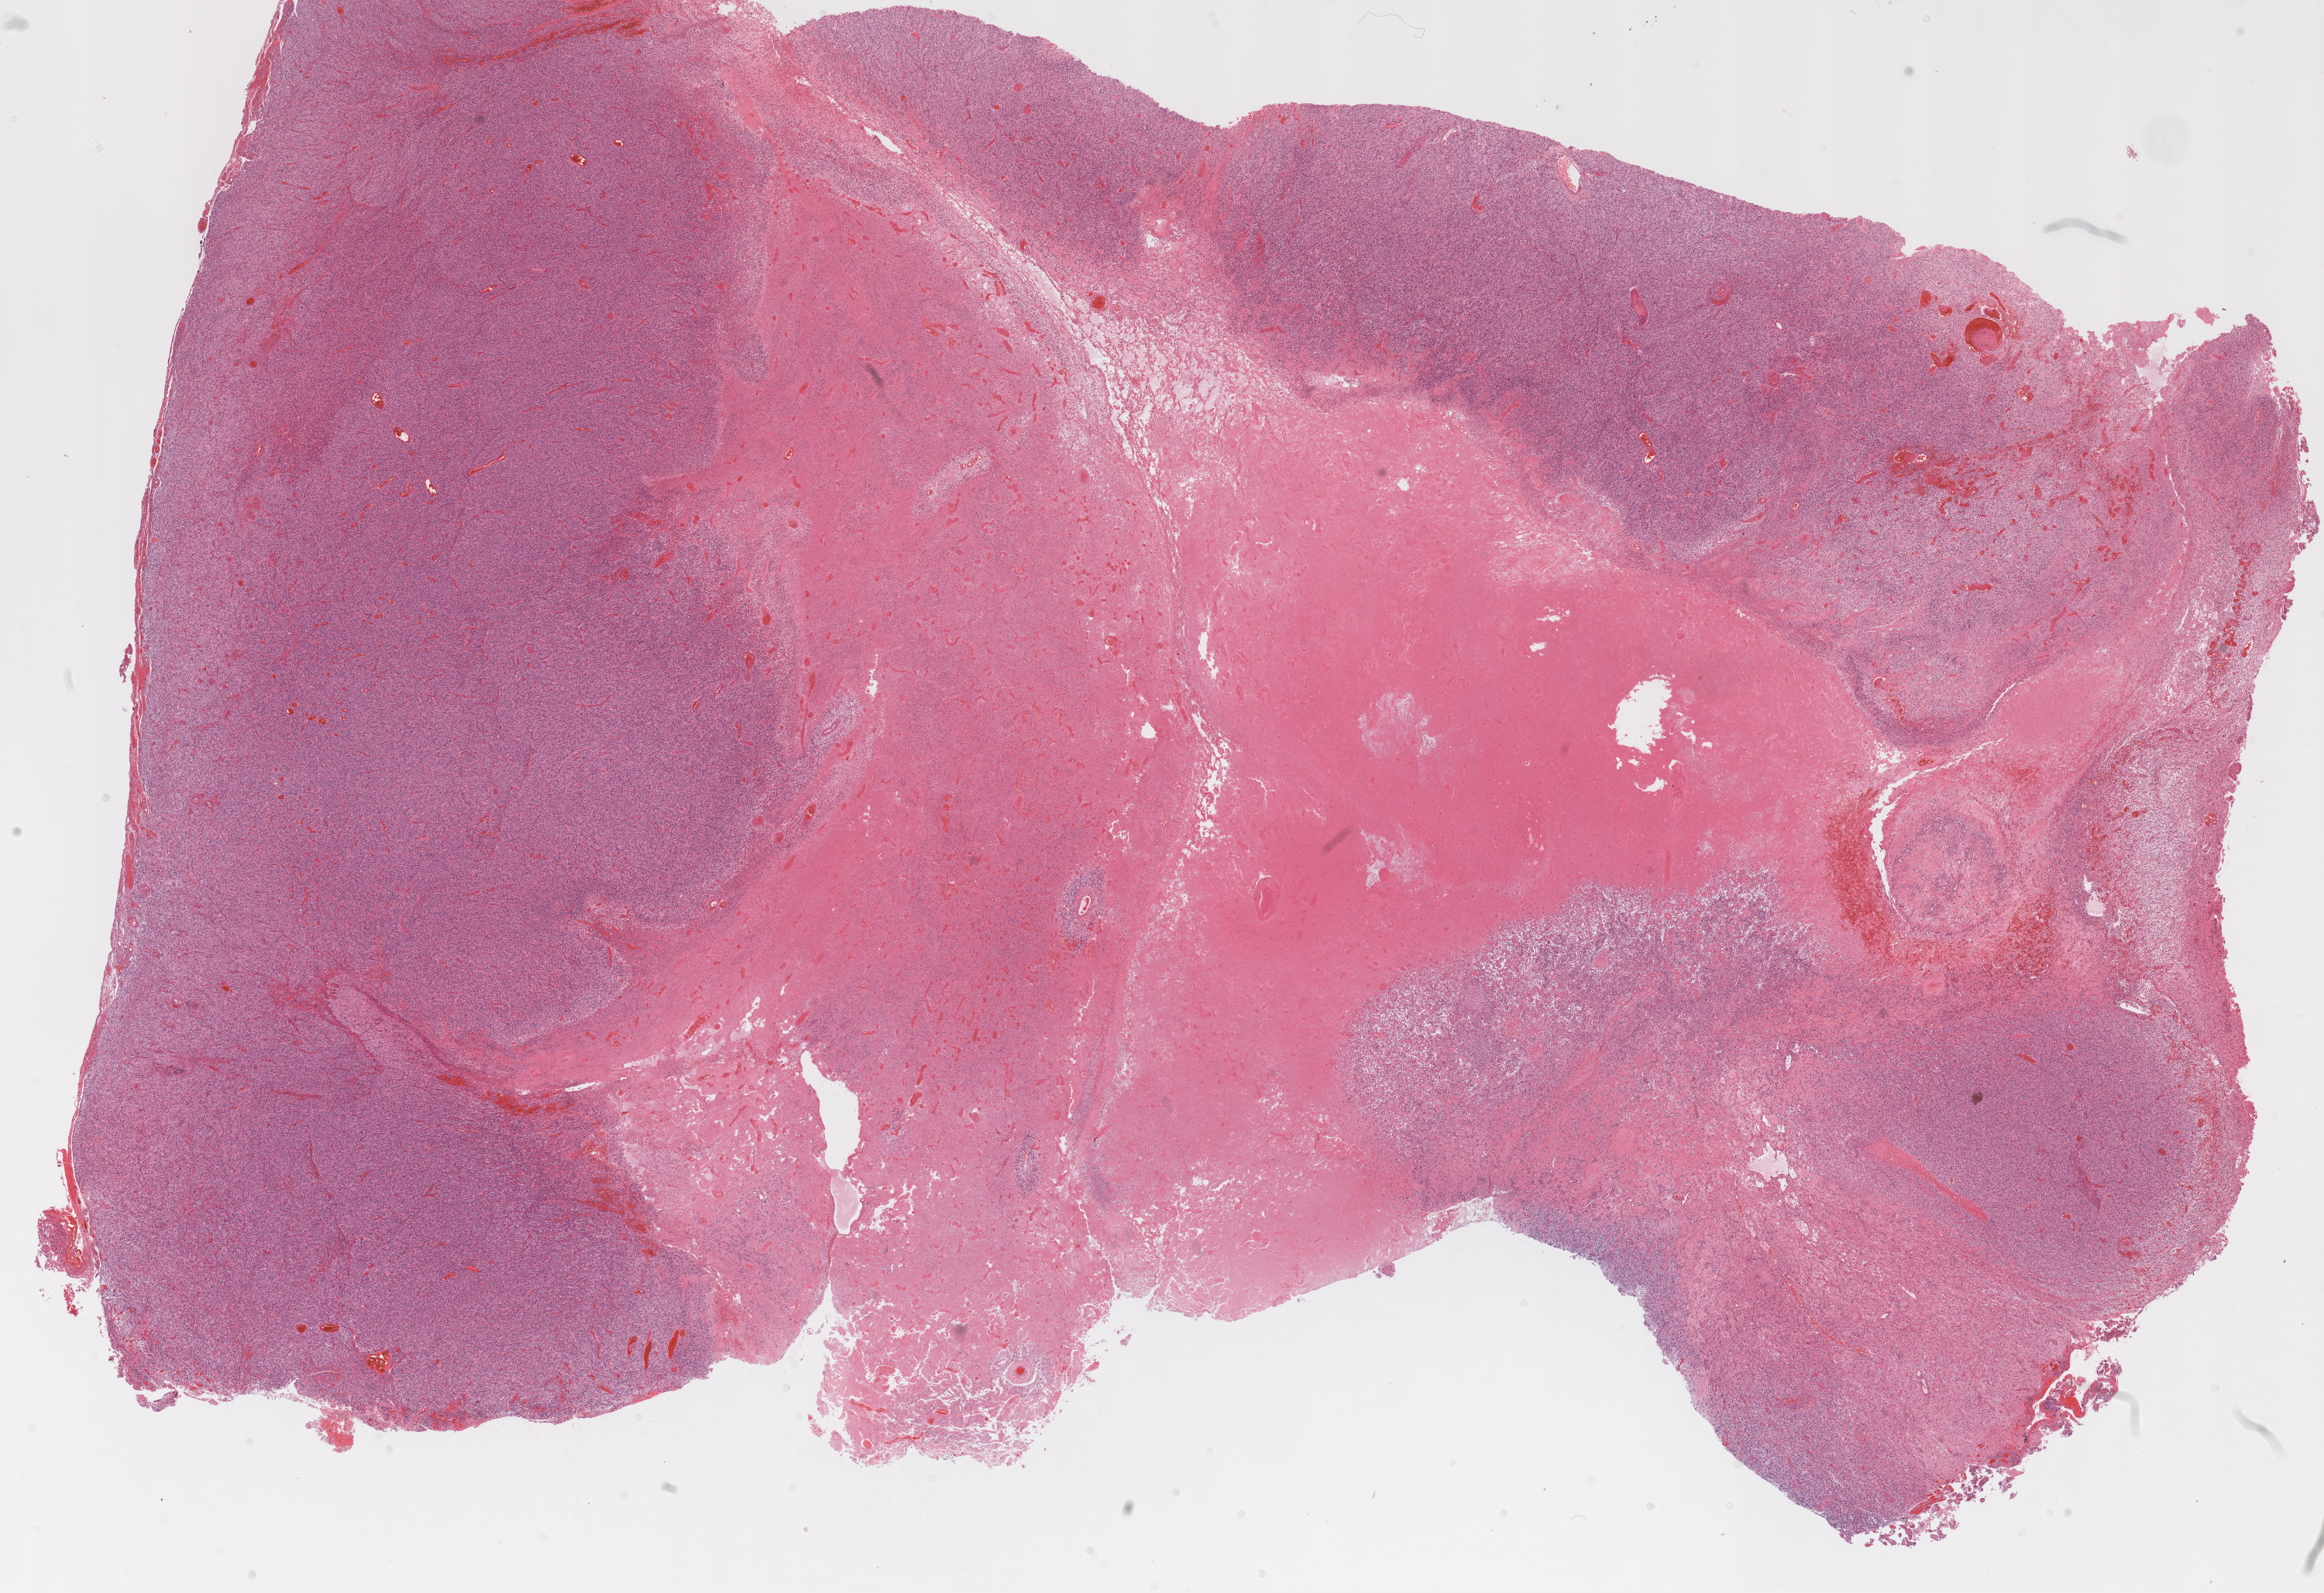
Digitized H&E-stained tissue section (whole slide) — a low-resolution overview of the entire scanned area, about 24.1 x 16.5 mm; formalin-fixed paraffin-embedded (FFPE) diagnostic section; sample: primary tumour, brain. Female patient; age at initial diagnosis 63 years.
Pathologic diagnosis: Glioblastoma.